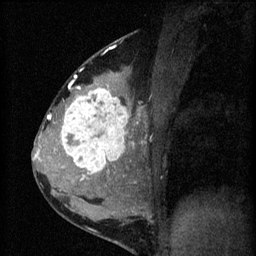
Breast MRI (dynamic contrast-enhanced), one sagittal slice; 3 images stored at this slice position (order not interpretable as contrast timing); 1.5 T; TE 4.2 ms, TR 8.2 ms; 2 mm slice thickness; 256 × 256 image matrix, field of view 180 × 180 mm. Patient: female, 37 years.
Structures marked on this image (semi-automatic segmentation, software-assisted and operator-edited):
- analysis volume of interest (the breast-tissue region the enhancement analysis was run in; not a lesion): box from (x=53, y=78) to (x=140, y=181) px
- tumour enhancement mask (voxels above the 70 % enhancement threshold inside the analysis volume of interest): (x=61, y=78)–(x=140, y=181)